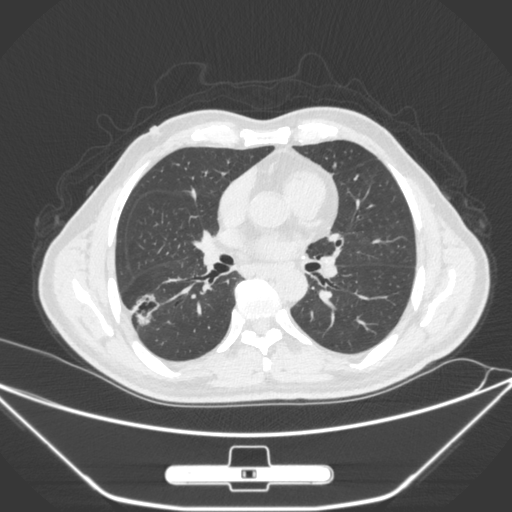
Chest CT, one axial slice. Position 149 of 310 along the scan axis. 120 kVp. Lung window (W 1500 / L -600 HU). 512 × 512 image matrix. Patient: male, 71 years. Case-level facts recorded for this patient, not image findings: clinical TNM (as recorded): T1c N0 M0; histopathological grade: G2.
Structures marked on this image (bounding box drawn by a radiologist):
- lung tumour (recorded histology: adenocarcinoma): bounding box <128,290,166,336> (left, top, right, bottom; pixels)